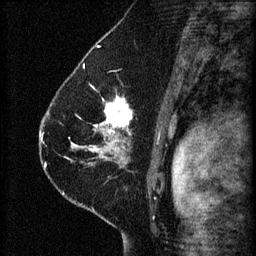
Breast MRI (dynamic contrast-enhanced), one sagittal slice; slice 41 of 60 in the series (ordered by position); 3 images stored at this slice position (order not interpretable as contrast timing); 1.5 T; TE 4.2 ms, TR 8.2 ms; 256 × 256 image matrix, field of view 180 × 180 mm. Patient: female, 41 years.
Structures marked on this image (semi-automatic segmentation, software-assisted and operator-edited):
- analysis volume of interest (the breast-tissue region the enhancement analysis was run in; not a lesion): bounding box <67,94,165,173> (left, top, right, bottom; pixels)
- tumour enhancement mask (voxels above the 70 % enhancement threshold inside the analysis volume of interest): <73,96,132,165>